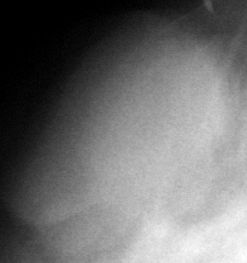
Crop from a digitized film mammogram around one marked abnormality, right breast, CC view.
Mass, shape oval, margins circumscribed; BI-RADS assessment category 3; pathology (as recorded): benign.